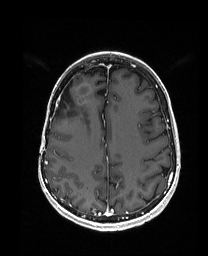
Brain MRI from a brain-tumour surgery series, one axial slice; T1-weighted post-contrast; 1 mm slice thickness; 208 × 256 image matrix, field of view 203 × 250 mm. Case-level facts recorded for this patient, not image findings: histopathology: Metastatic Carcinoma from Breast primary; tumour location: Right Frontal.
Annotated regions visible in this slice (expert manual segmentation):
- previous resection cavity: bounding box (x1, y1, x2, y2) in pixels: (55, 83, 72, 115)
- tumour: (75, 82, 91, 112)